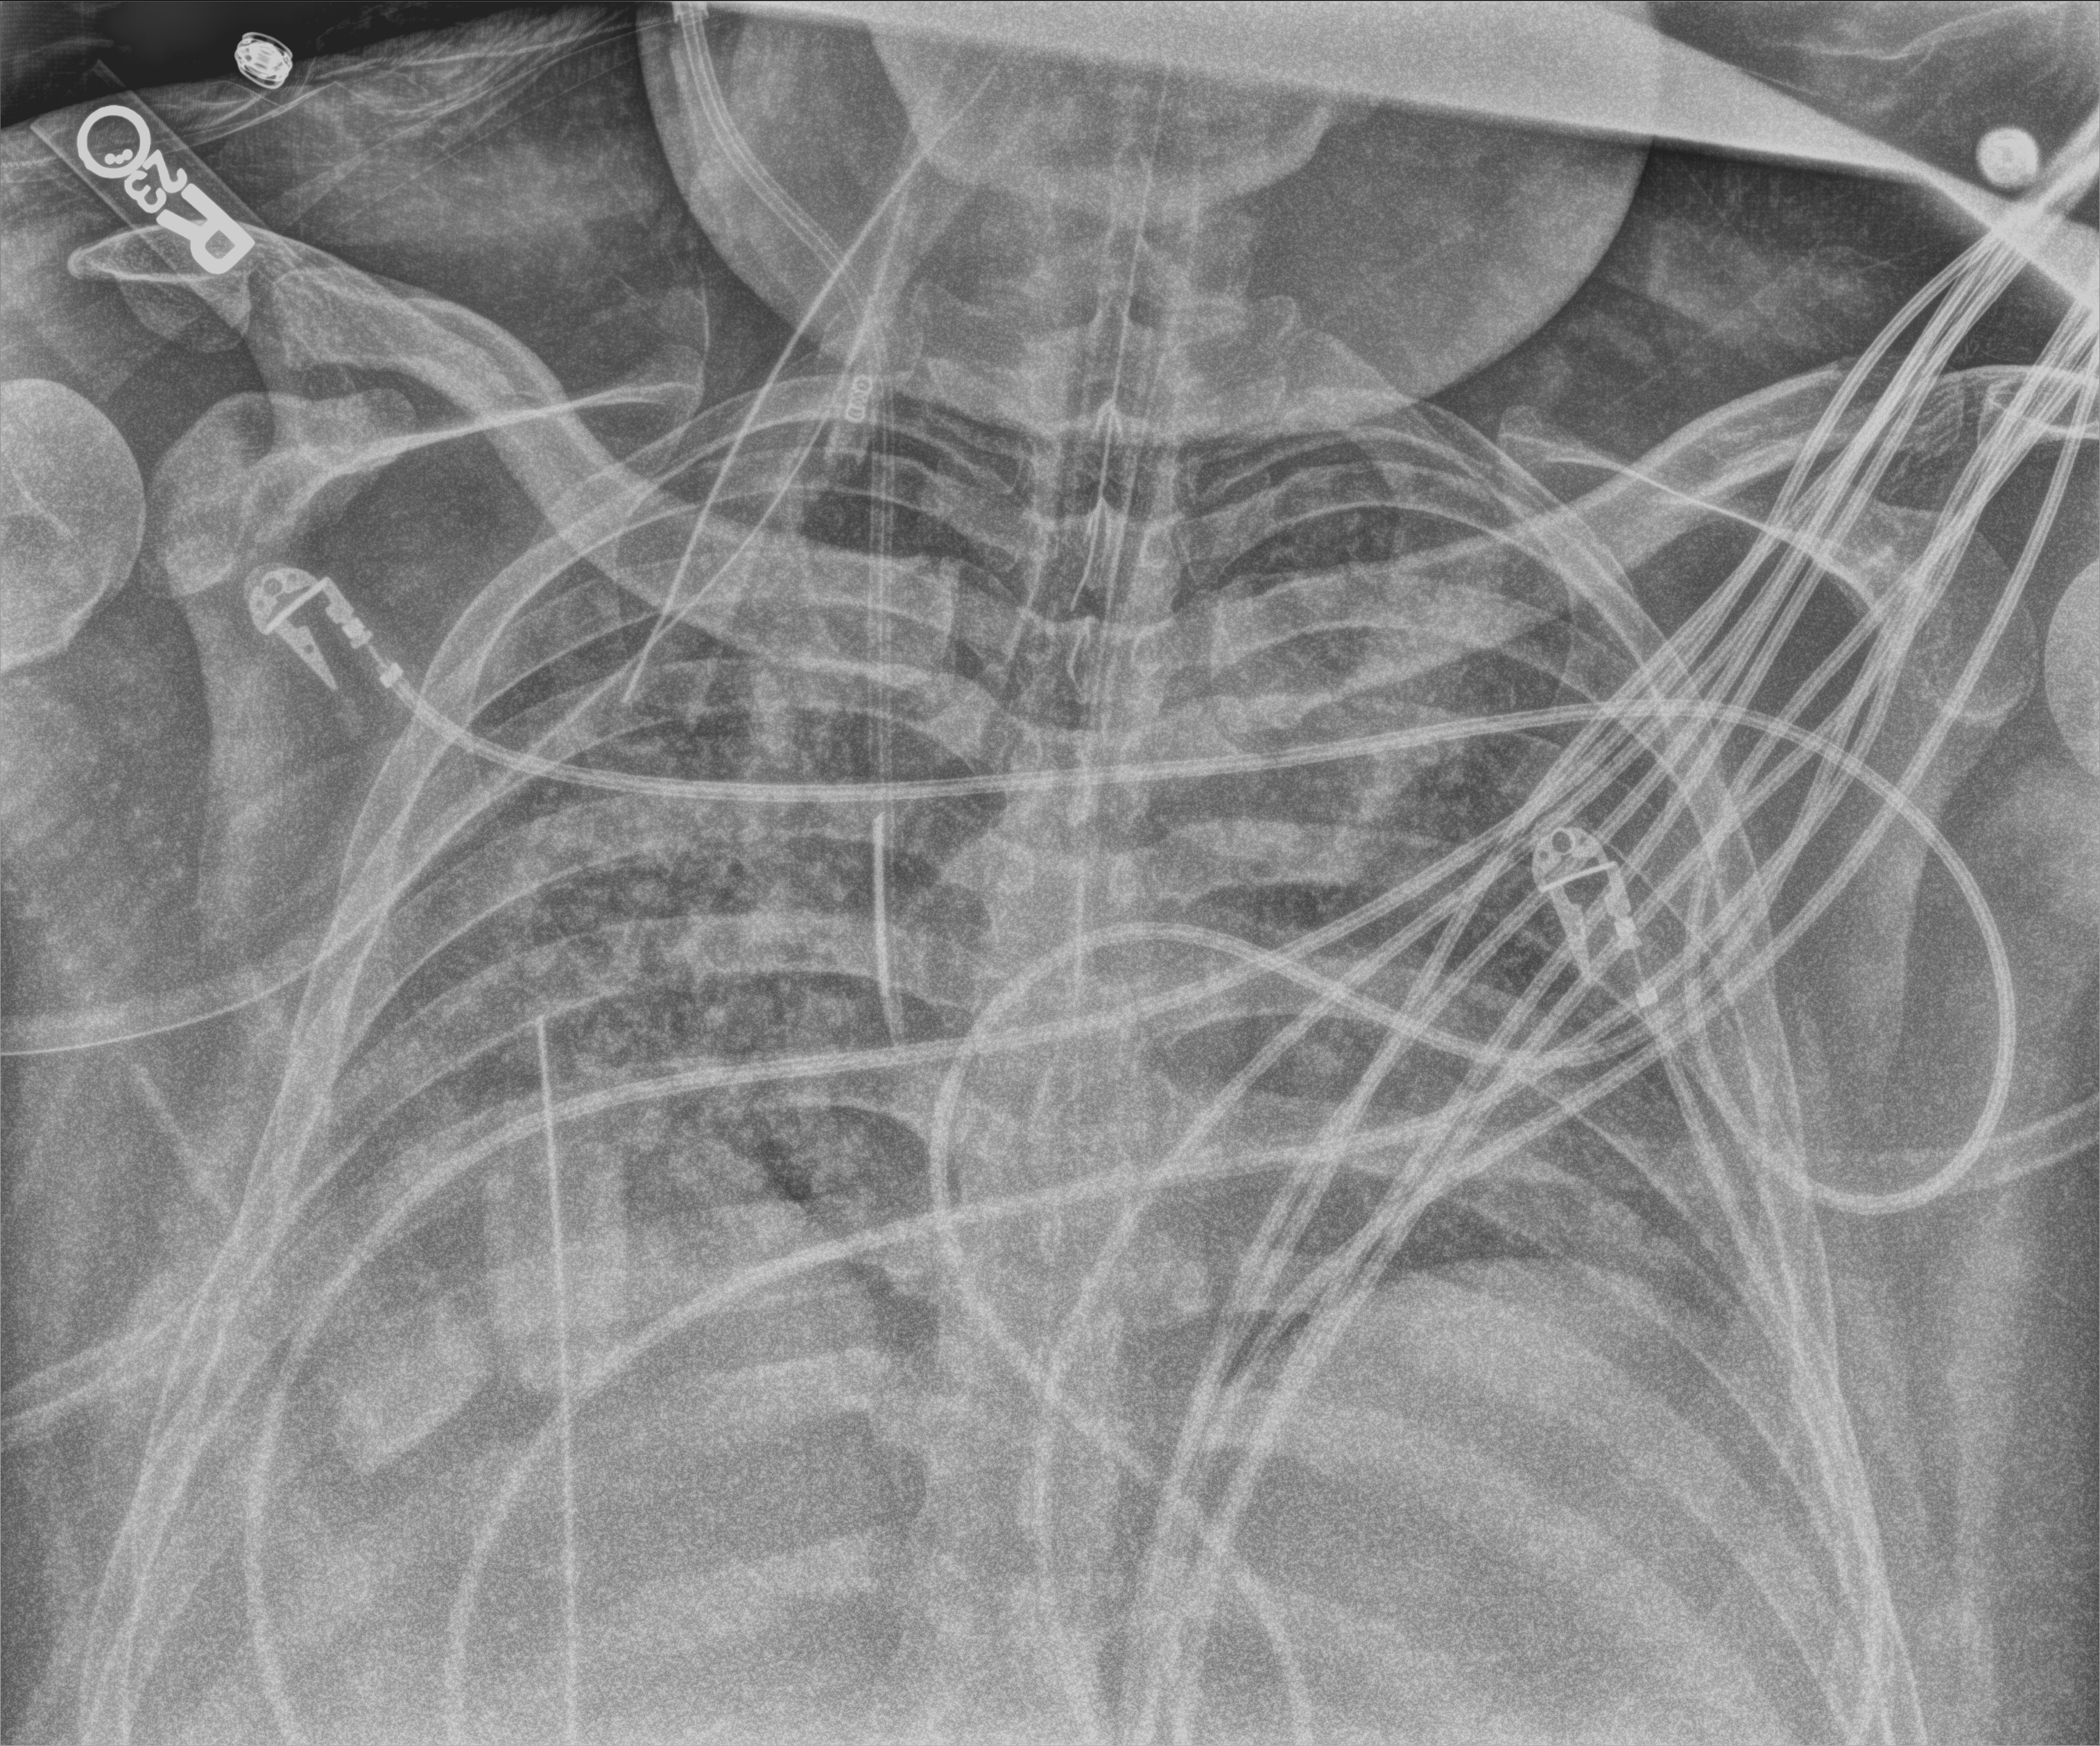
Bedside chest radiograph (computed radiography), anteroposterior (AP) projection. Adult patient hospitalised with COVID-19, age 18–59 years.
Admission-level facts for this patient (not findings on this image; timing relative to this image not recorded): mechanically ventilated during this hospital stay: yes; hypertension (admission record): no.